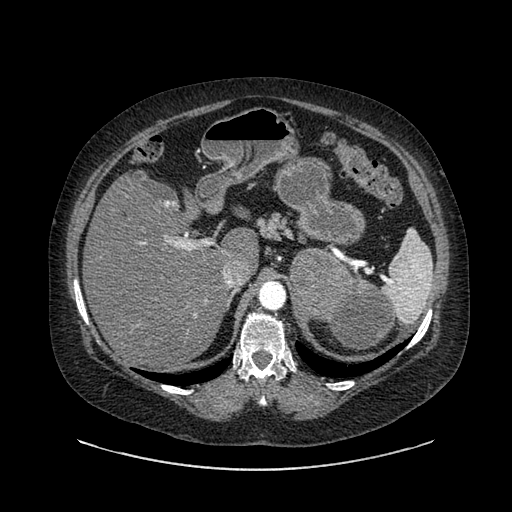
Contrast-enhanced abdominal CT, one axial slice; position 605 of 769 along the scan axis; reconstruction kernel SOFT; intravenous contrast given; soft-tissue window (W 400 / L 40 HU); 0.62 mm slice thickness; 512 × 512 image matrix, field of view 460 × 460 mm. Female patient, age 61 years. Case-level facts recorded for this patient, not image findings: diagnosis: adrenocortical carcinoma; tumour side: left adrenal; tumour size at pathology: 13 cm; Ki-67 index: 79 %; stage (as recorded): 2.
Annotated regions visible in this slice (semi-automatically segmented with operator editing):
- mass: bounding box (x1, y1, x2, y2) in pixels: (289, 250, 396, 350)